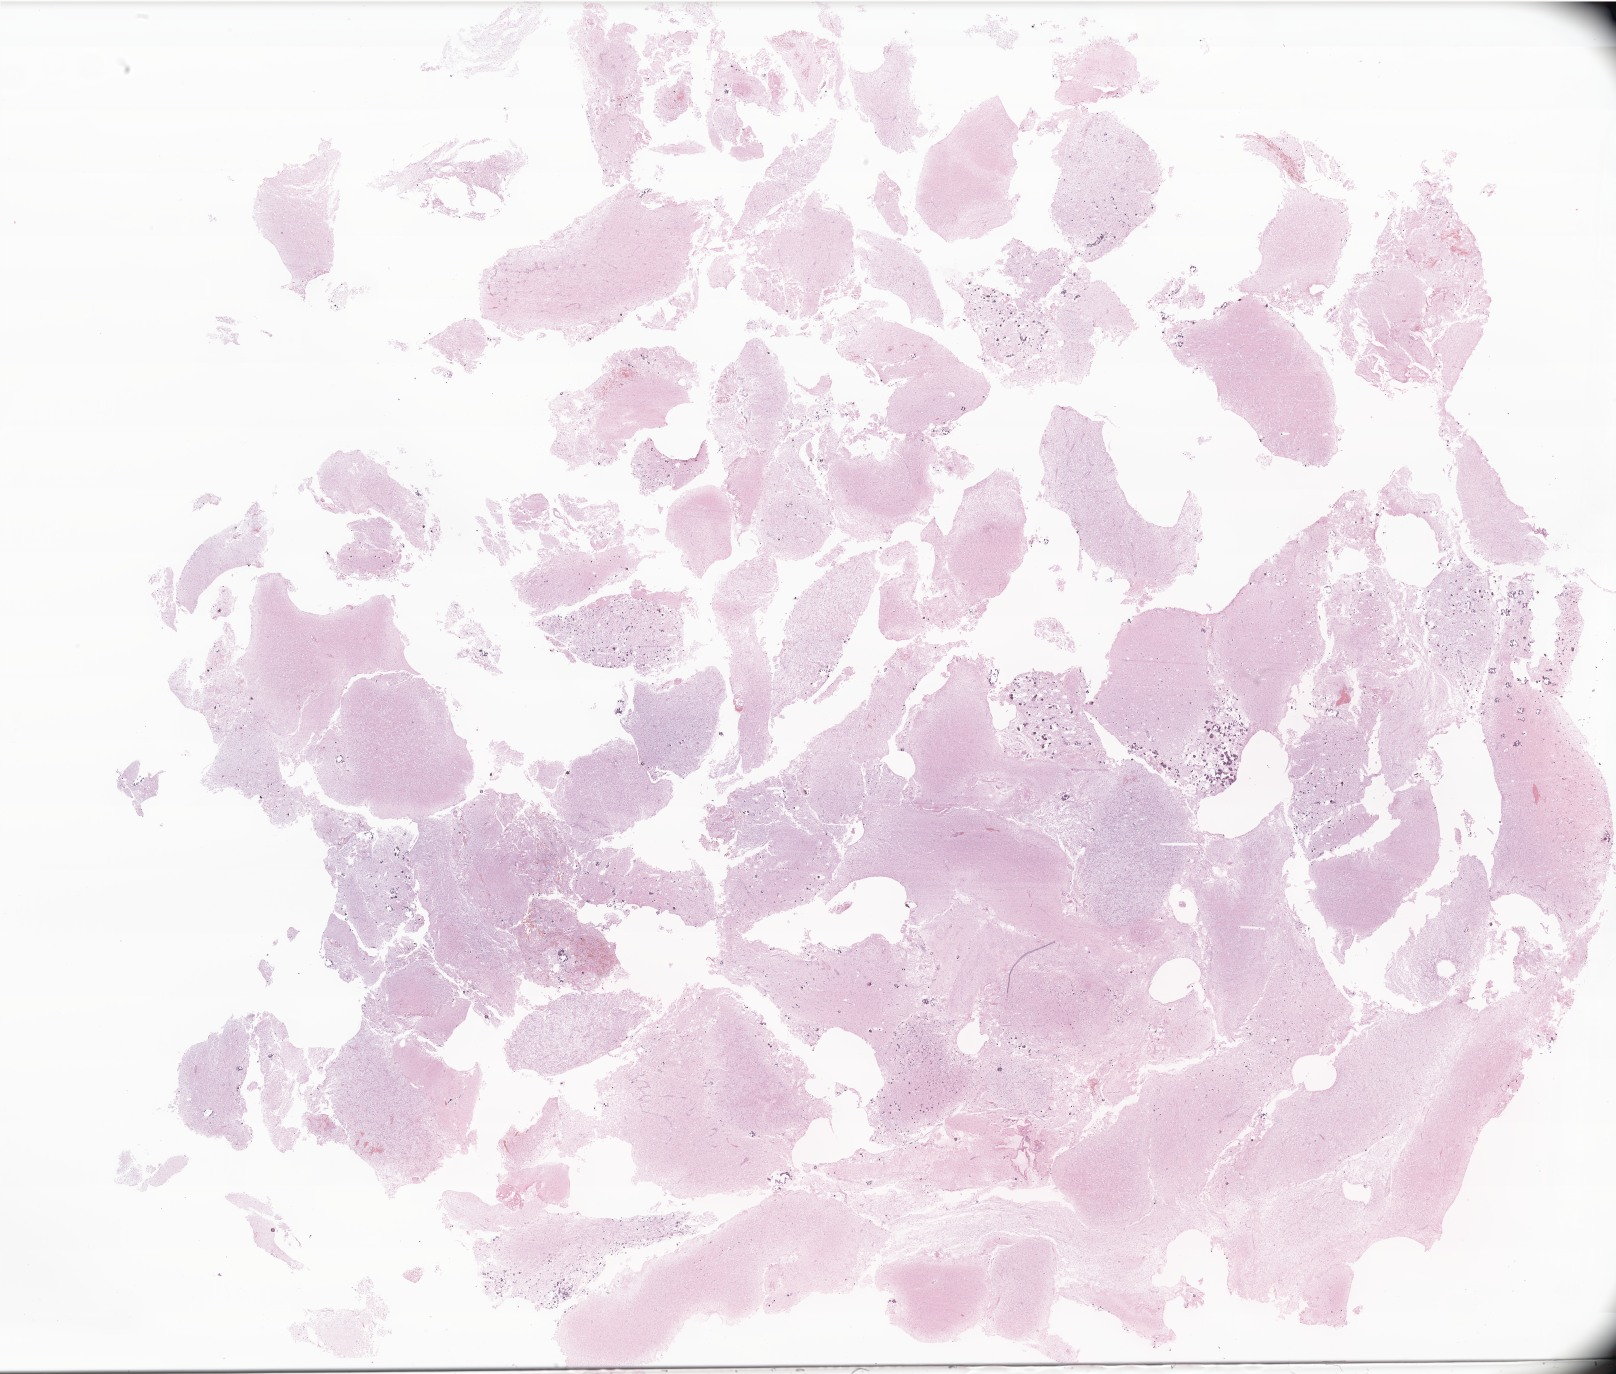
Whole-slide image, haematoxylin and eosin stain of tumor tissue from the brain, whole scanned area (about 27.3 x 23.2 mm) shown as a low-resolution overview; FFPE section. Female patient, age 146 months.
Diagnosis (ICD-O-3 morphology term): Pilocytic astrocytoma.